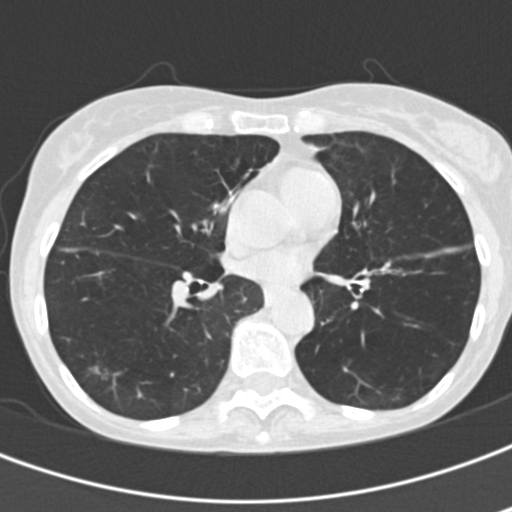
Low-dose screening chest CT, axial slice, second annual screen, lung window (W 1500 / L -600 HU), standard (soft-tissue) reconstruction kernel (B30f). Female participant, aged 68 years at enrolment.
• Lesion marked by an expert reader, bounding box <75,351,123,387> (left, top, right, bottom; pixels).
• Reader record for this screening exam (exam-level; its link to the box is not recorded): non-calcified nodule or mass ≥4 mm, right lower lobe, 9 × 7 mm, spiculated (stellate) margins, soft tissue attenuation, pre-existing on the prior screen: yes; interval growth: yes.
• Participant outcome: lung cancer diagnosed 659 days after this screen — squamous cell carcinoma, NOS, right lower lobe, stage IA (AJCC 6th edition).